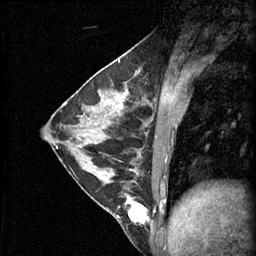
Breast MRI (dynamic contrast-enhanced), one sagittal slice; position 23 of 60 along the scan axis; 3 images stored at this slice position (order not interpretable as contrast timing); 1.5 T; TE 4.2 ms, TR 11 ms; 256 × 256 image matrix, field of view 180 × 180 mm. Female patient, age 29 years.
Structures marked on this image (semi-automatically segmented with operator editing):
- analysis volume of interest (the breast-tissue region the enhancement analysis was run in; not a lesion): box from (x=93, y=164) to (x=153, y=229) px
- tumour enhancement mask (voxels above the 70 % enhancement threshold inside the analysis volume of interest): (x=117, y=196)–(x=149, y=223)